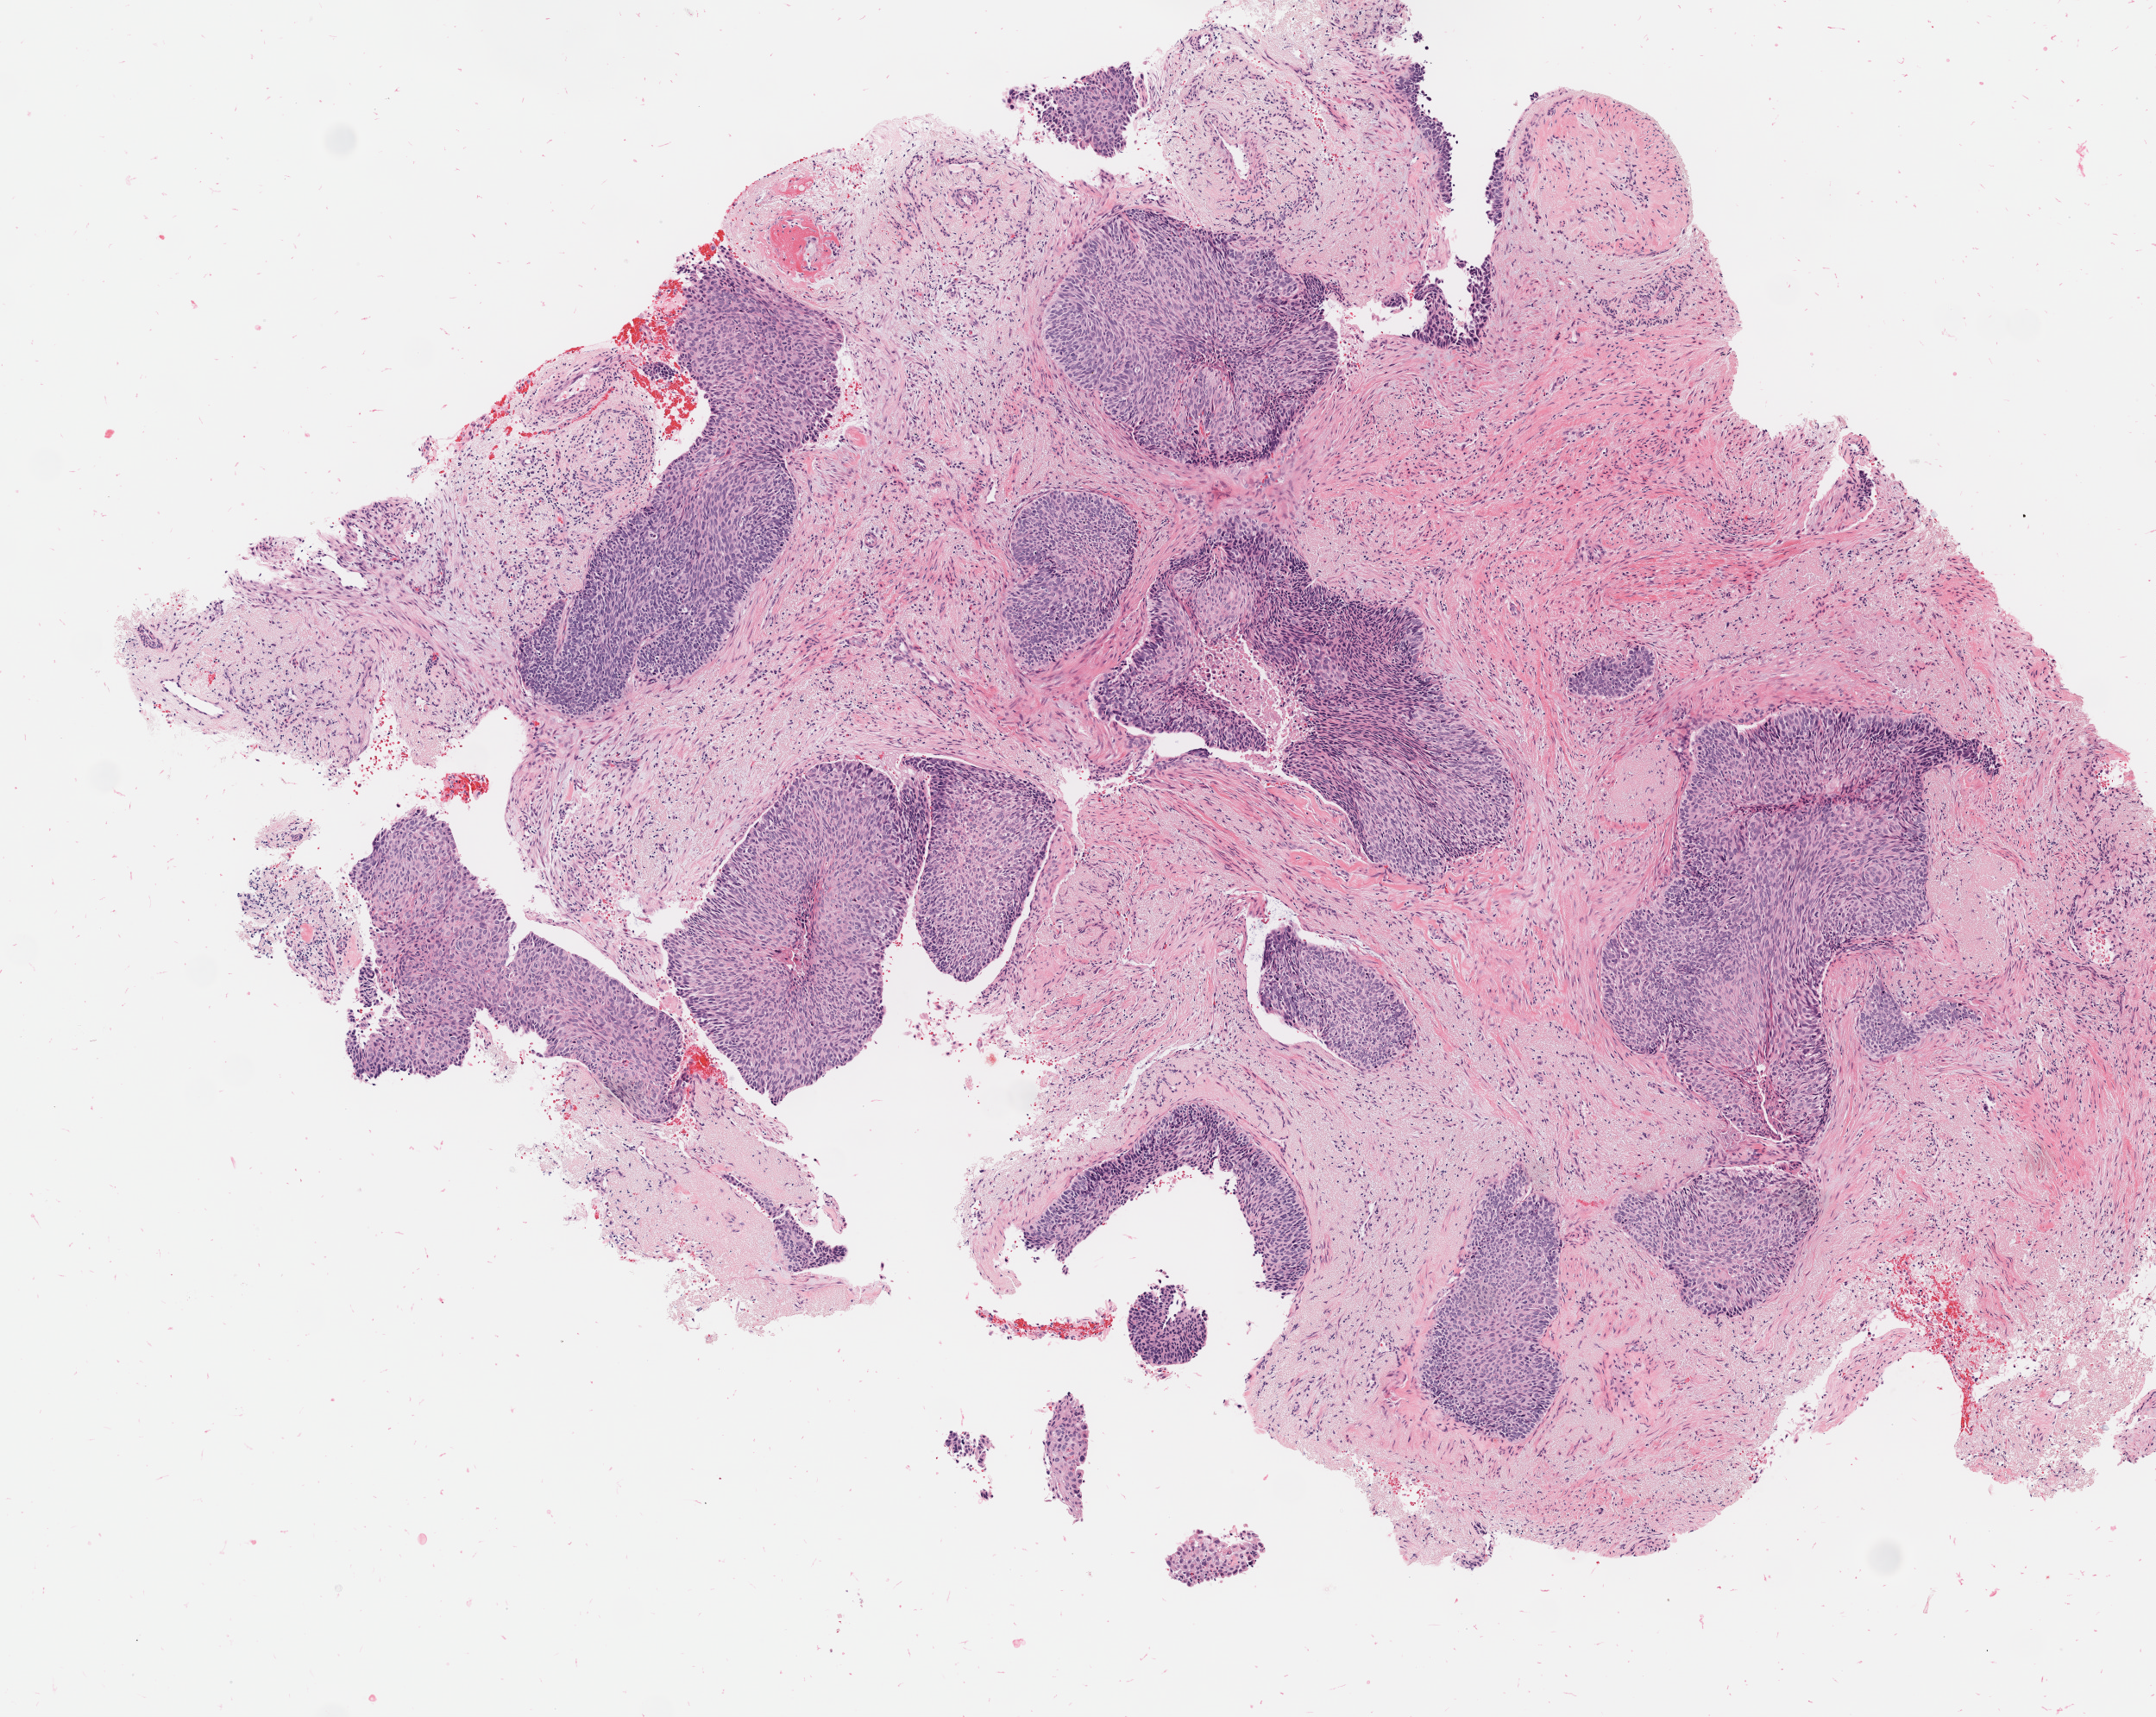
Digitized haematoxylin and eosin-stained section, low-resolution overview of the scanned area, about 5.0 x 4.0 mm. Tumor tissue. Site: cervix. Female patient, aged 48.
- diagnosis: Squamous cell carcinoma, large cell, nonkeratinizing, NOS